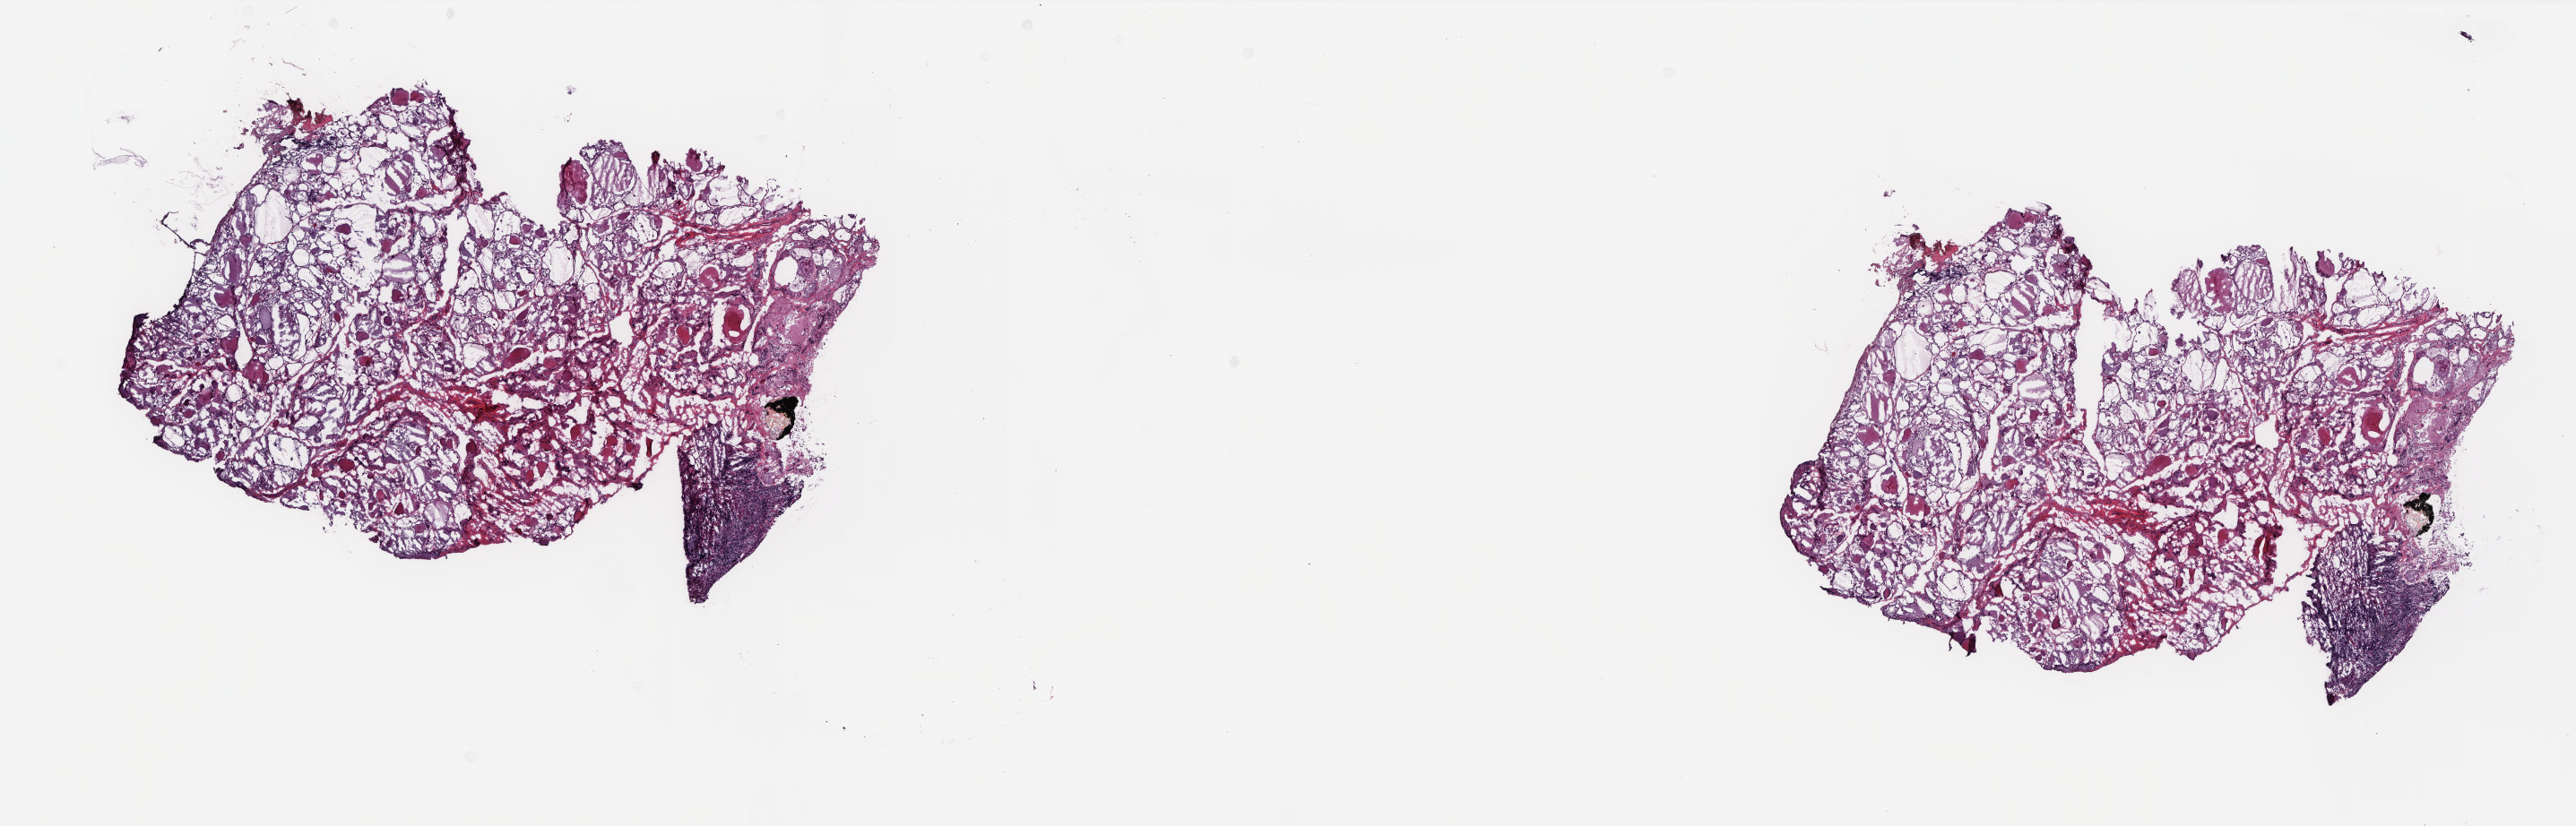
Digitized H&E-stained tissue section (whole slide) — whole scanned area (about 23.0 x 7.4 mm, acquisition: 20x scan) shown as a low-resolution overview. Frozen section from the top of the tissue portion. Sample: solid tissue normal (non-tumour tissue), thyroid. Female, age 45 years at initial diagnosis. Composition of this section per pathologist review: tumour cells 0%, tumour nuclei 0%, normal cells 100%, stromal cells 0%, necrosis 0%. Inflammatory infiltration, as recorded: lymphocyte infiltration 0%, monocyte infiltration 0%, neutrophil infiltration 0%.
This section: solid tissue normal sample (biorepository sample class). Patient diagnosis: Papillary adenocarcinoma, NOS (thyroid gland).